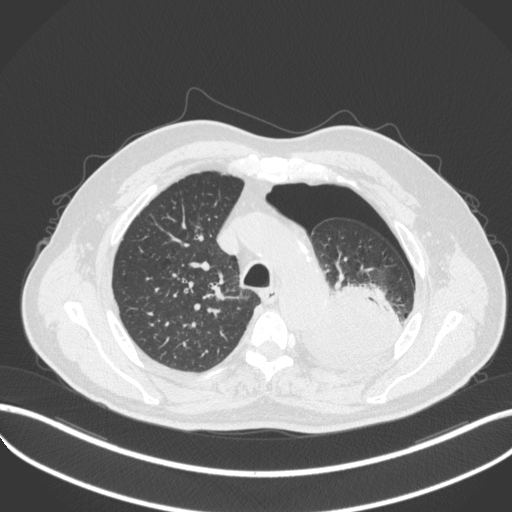
Chest CT, one axial slice; slice 381 of 466 in the series (ordered by position); reconstruction kernel B31f; lung window (W 1500 / L -600 HU); 1 mm slice thickness; 512 × 512 image matrix, field of view 400 × 400 mm. Male patient, age 76 years. Case-level facts recorded for this patient, not image findings: clinical TNM (as recorded): T3 N0 M1b.
Annotated regions visible in this slice (rectangle marked by the reading radiologist):
- lung tumour (recorded histology: adenocarcinoma): bounding box [x1, y1, x2, y2] px = [299, 275, 403, 371]